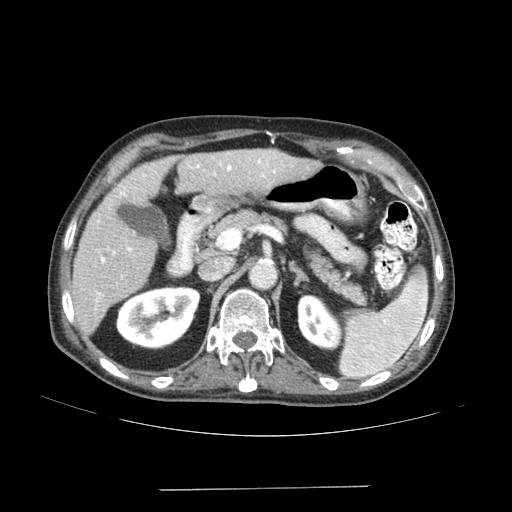
Contrast-enhanced abdominal CT (liver protocol), one axial slice; position 86 of 192 along the scan axis; reconstruction kernel SOFT; soft-tissue window (W 400 / L 40 HU); 2.5 mm slice thickness; 512 × 512 image matrix, field of view 400 × 400 mm. Case-level facts recorded for this patient, not image findings: diagnosis: hepatocellular carcinoma (patient treated with transarterial chemoembolisation; whether this scan precedes or follows treatment is not stated here); TNM stage (as recorded): Stage-IVA; Child-Pugh class: A; tumour differentiation: poorly differentiated; tumour nodularity: uninodular.
Structures marked on this image (semi-automatically segmented with operator editing):
- liver parenchyma outside the tumour (the mass and vessels are separate outlines, so this box may not span the whole liver): bounding box <72,150,320,332> (left, top, right, bottom; pixels)
- liver vessels: <96,159,276,301>